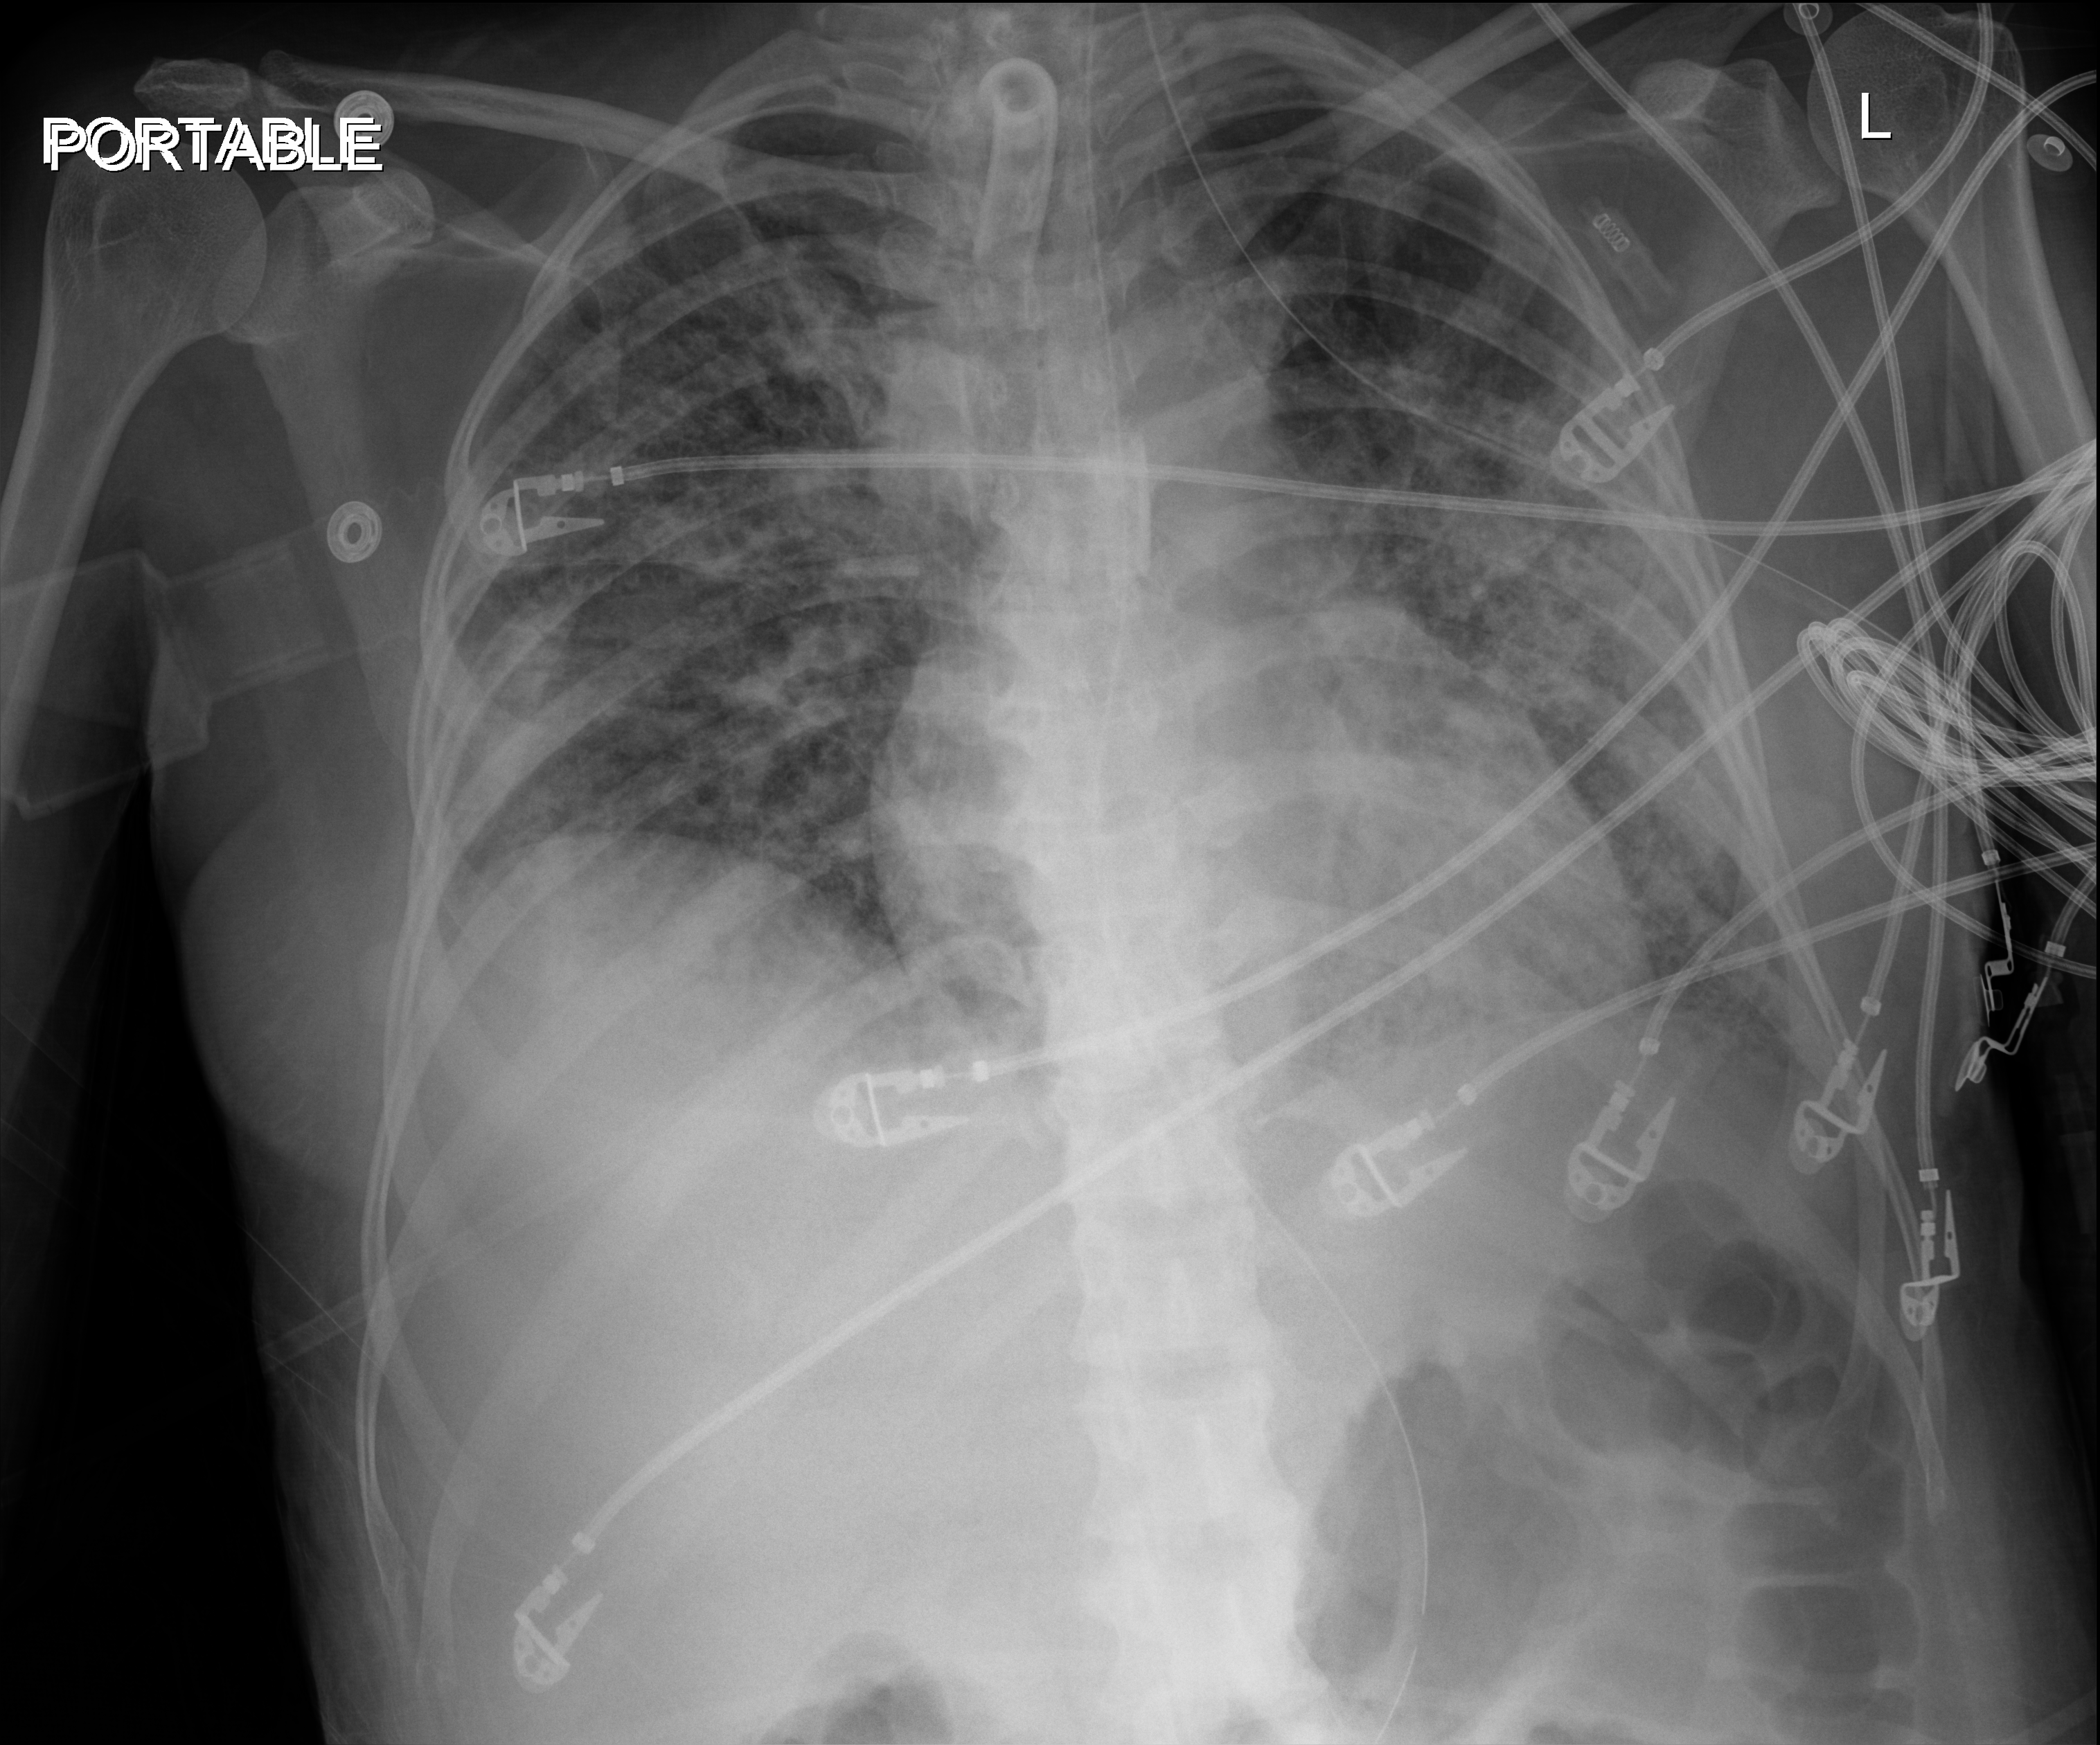
Bedside chest radiograph (digital radiography), anteroposterior (AP) projection. Female patient hospitalised with COVID-19, age 18–59 years.
Admission-level facts for this patient (not findings on this image; timing relative to this image not recorded):
- mechanically ventilated during this hospital stay: yes
- admitted to intensive care during this hospital stay: yes